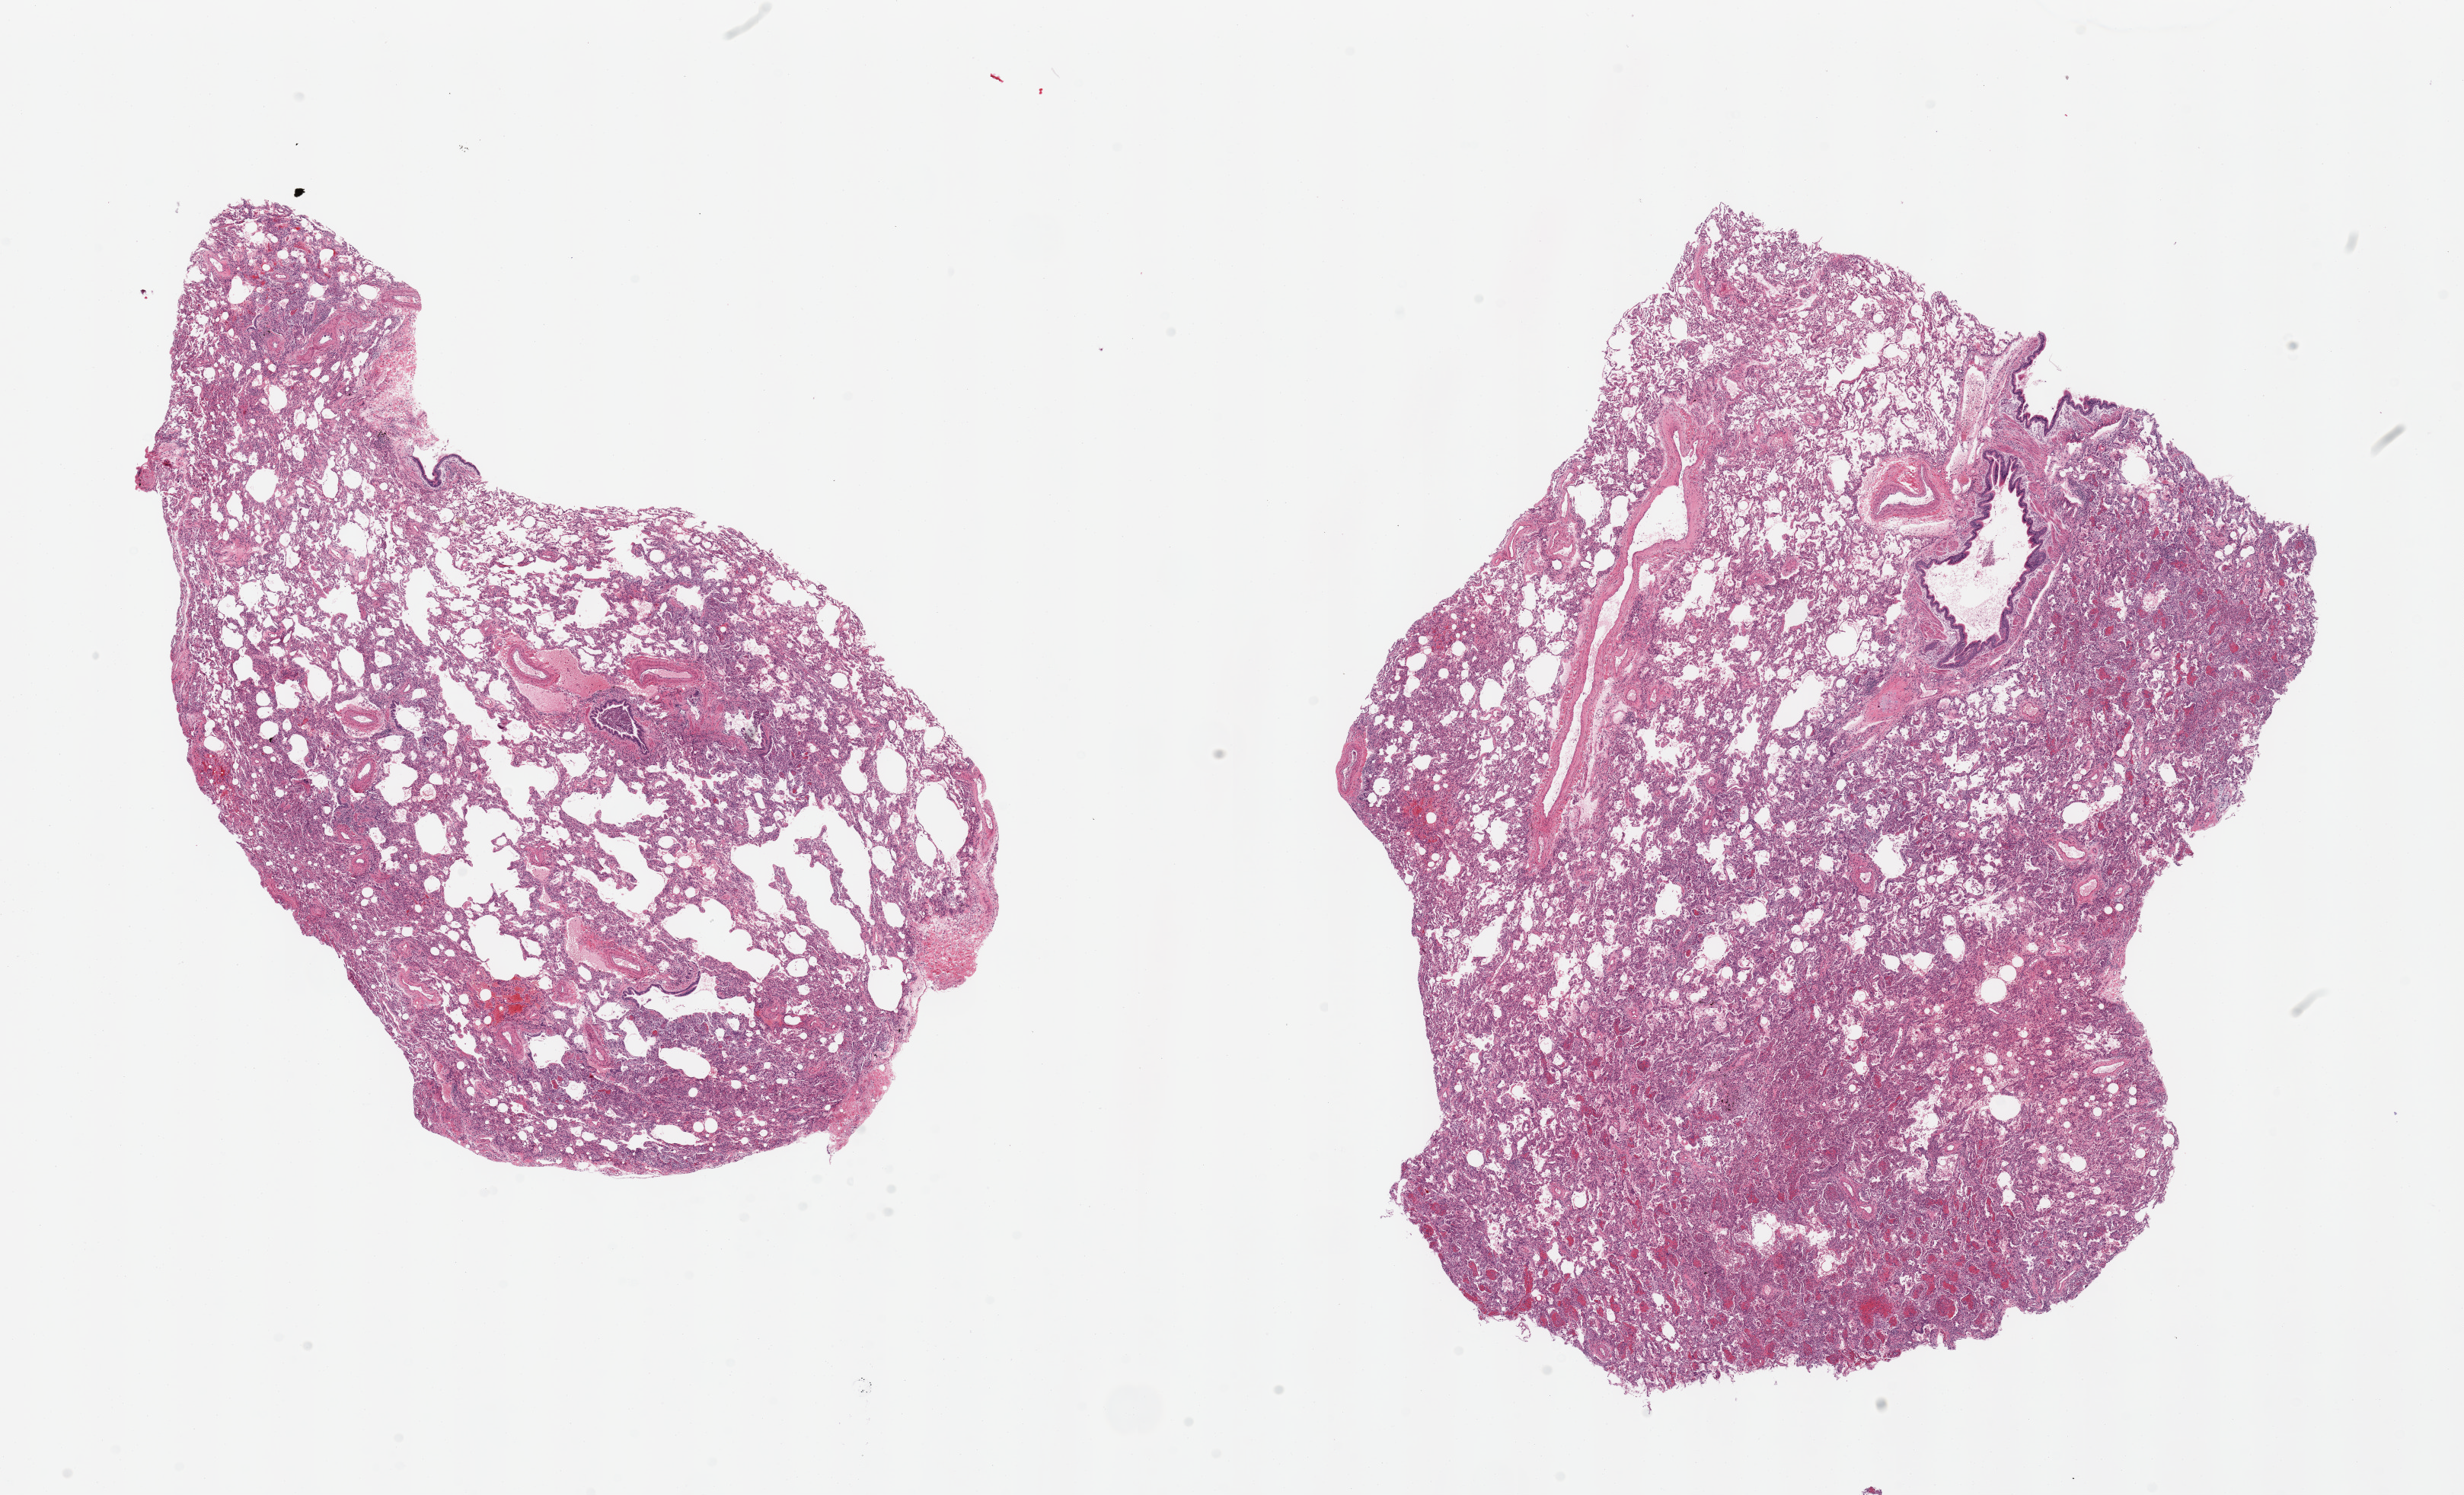
Whole-slide image, hematoxylin and eosin (H&E) stain — low-resolution overview of the scanned area, about 25.6 x 15.5 mm. PAXgene-fixed, paraffin-embedded tissue. Sampled site (target tissue): lung. Donor tissue sample.
Pathologist's review note for this sample: 2 pieces, patchy foci of acute pneumonia.